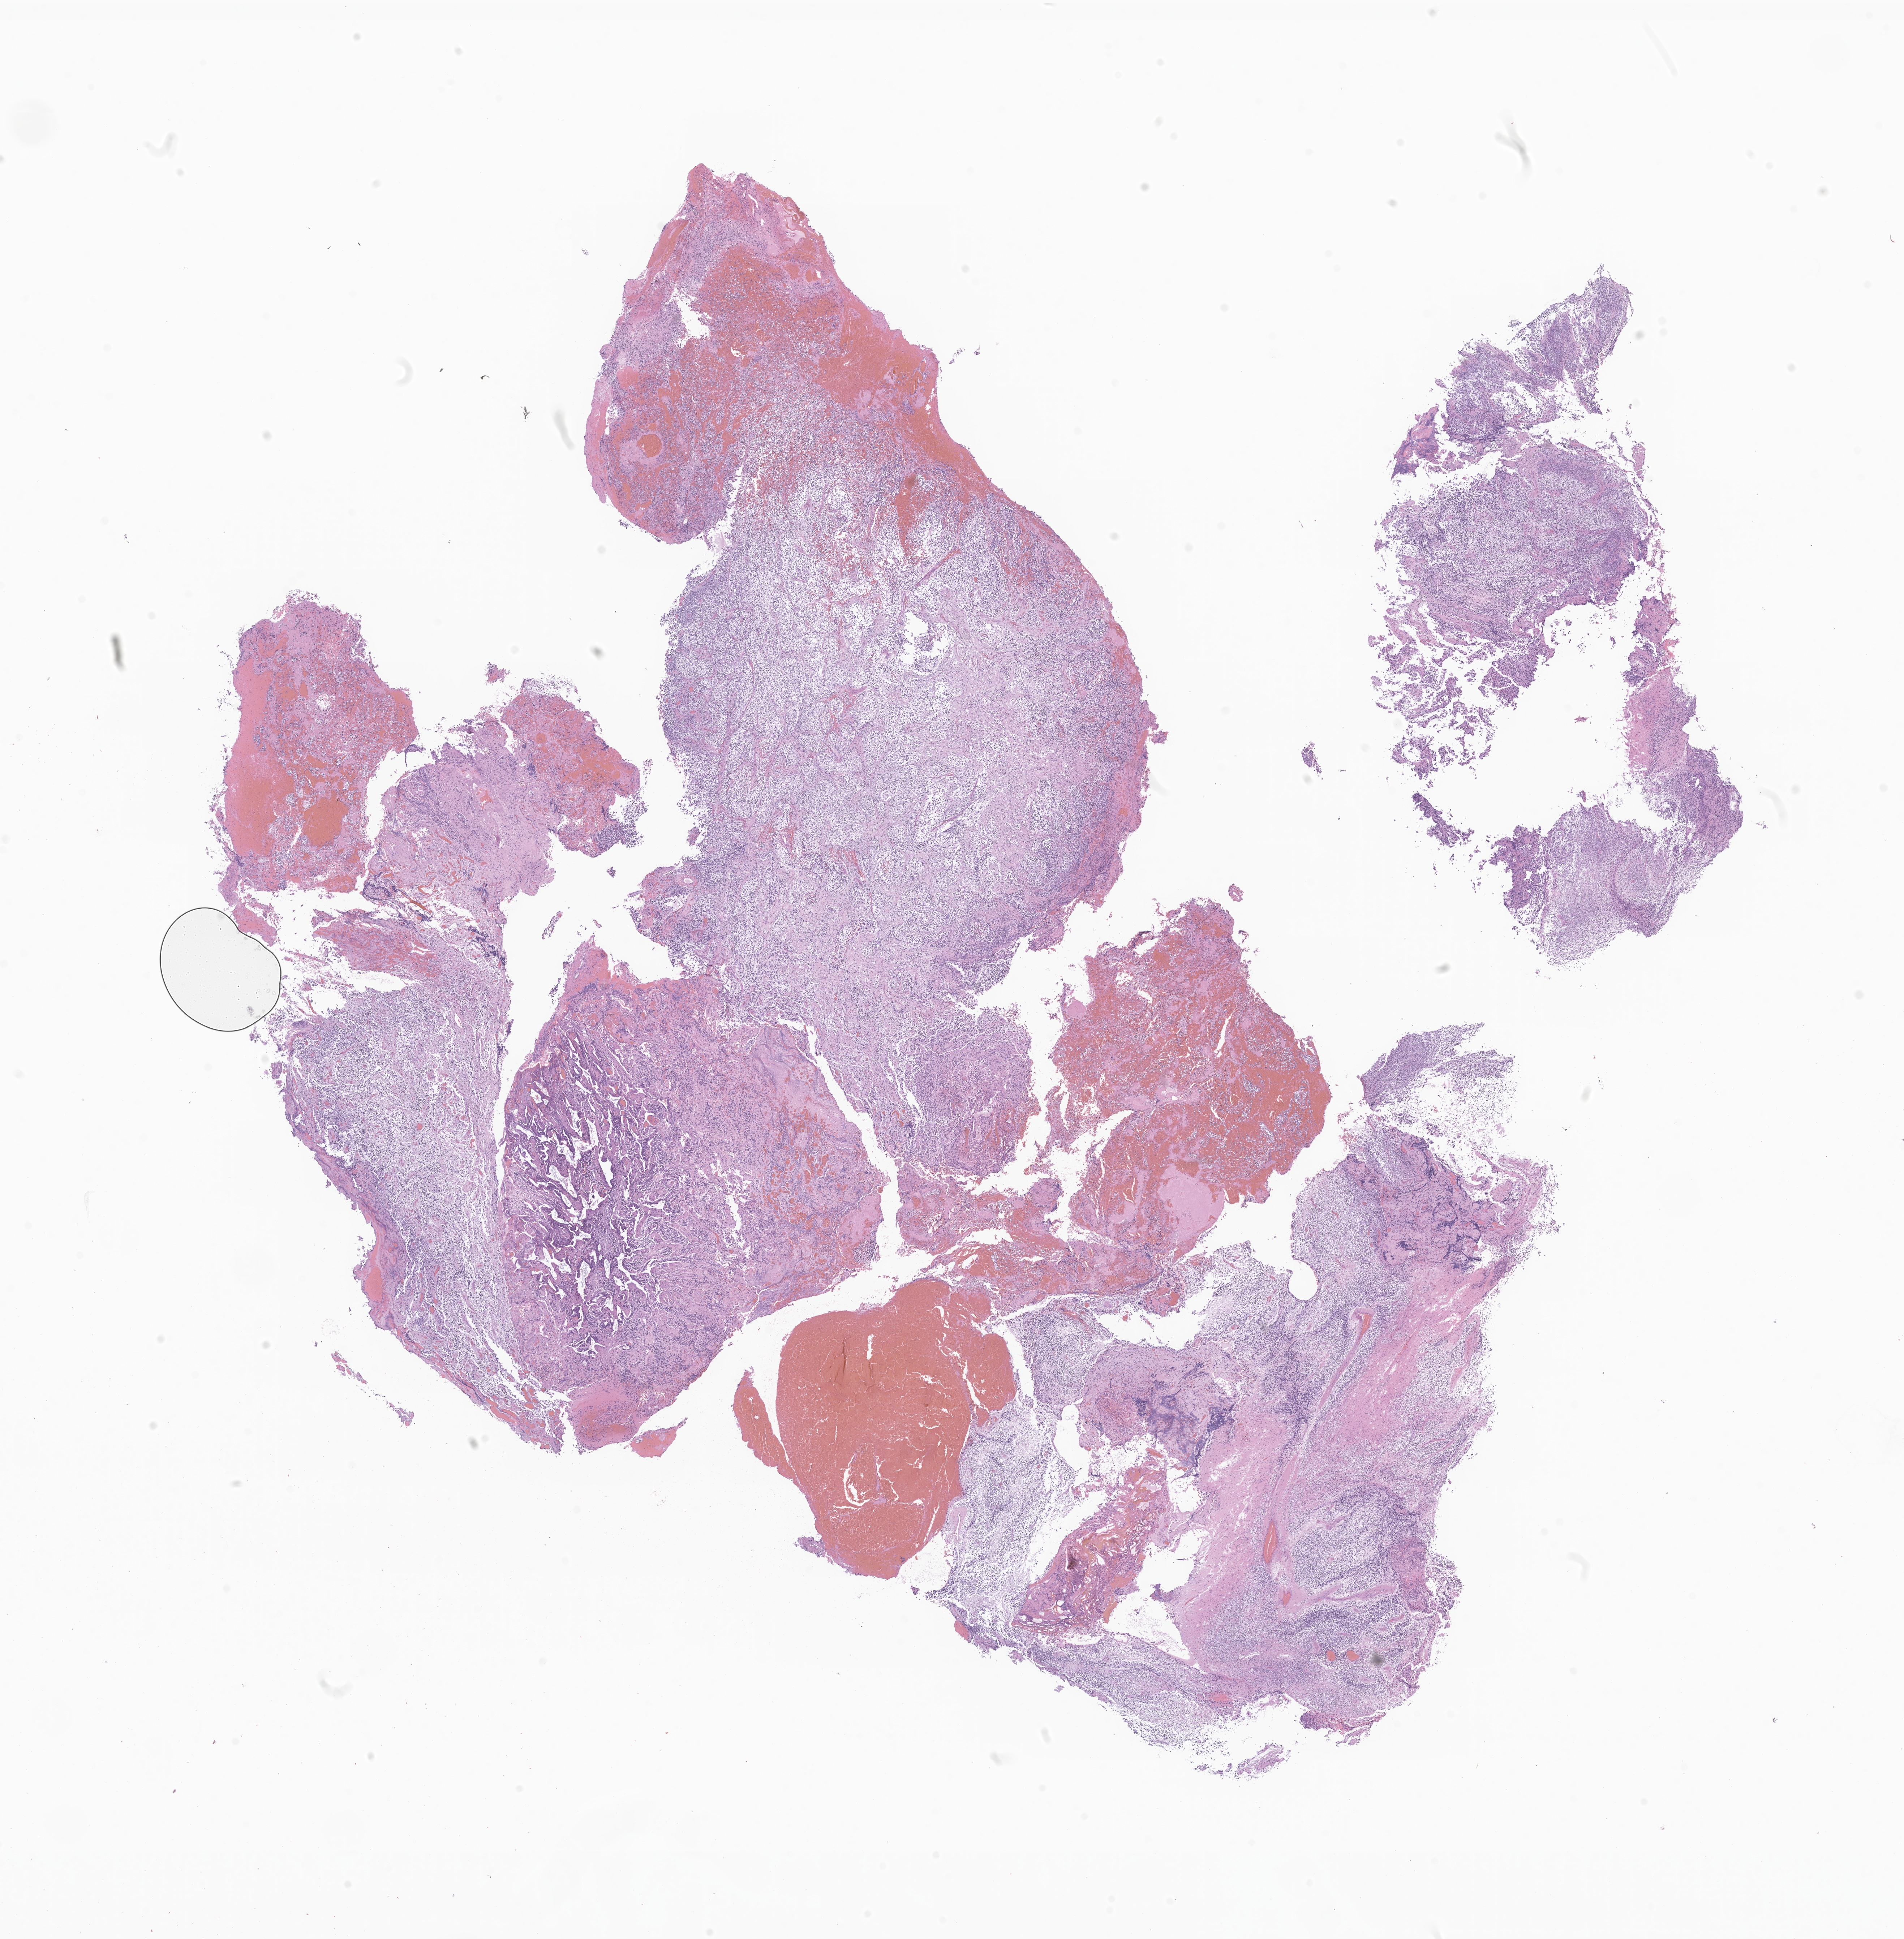
Haematoxylin and eosin whole-slide image of tumor tissue from the brain — low-resolution overview of the scanned area, about 22.2 x 22.6 mm, formalin-fixed, paraffin-embedded (FFPE) tissue. Patient: female, age 129 months (10 years 9 months).
• recorded diagnosis: Glioma, malignant